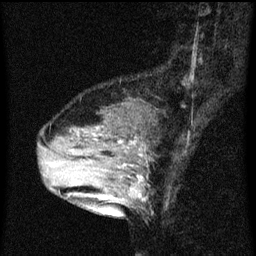
Breast MRI (dynamic contrast-enhanced), one sagittal slice. Slice 20 of 60 in the series (ordered by position). Dynamic contrast-enhanced series, image 2 of 3 at this slice position (ordered by acquisition). 1.5 T. TE 4.2 ms, TR 8 ms. 2 mm slice thickness. 256 × 256 image matrix. Female patient, age 33 years.
Outlined on this slice (semi-automatic segmentation, software-assisted and operator-edited):
- analysis volume of interest (the breast-tissue region the enhancement analysis was run in; not a lesion): box from (x=61, y=126) to (x=149, y=213) px
- tumour enhancement mask (voxels above the 70 % enhancement threshold inside the analysis volume of interest): (x=119, y=142)–(x=142, y=197)